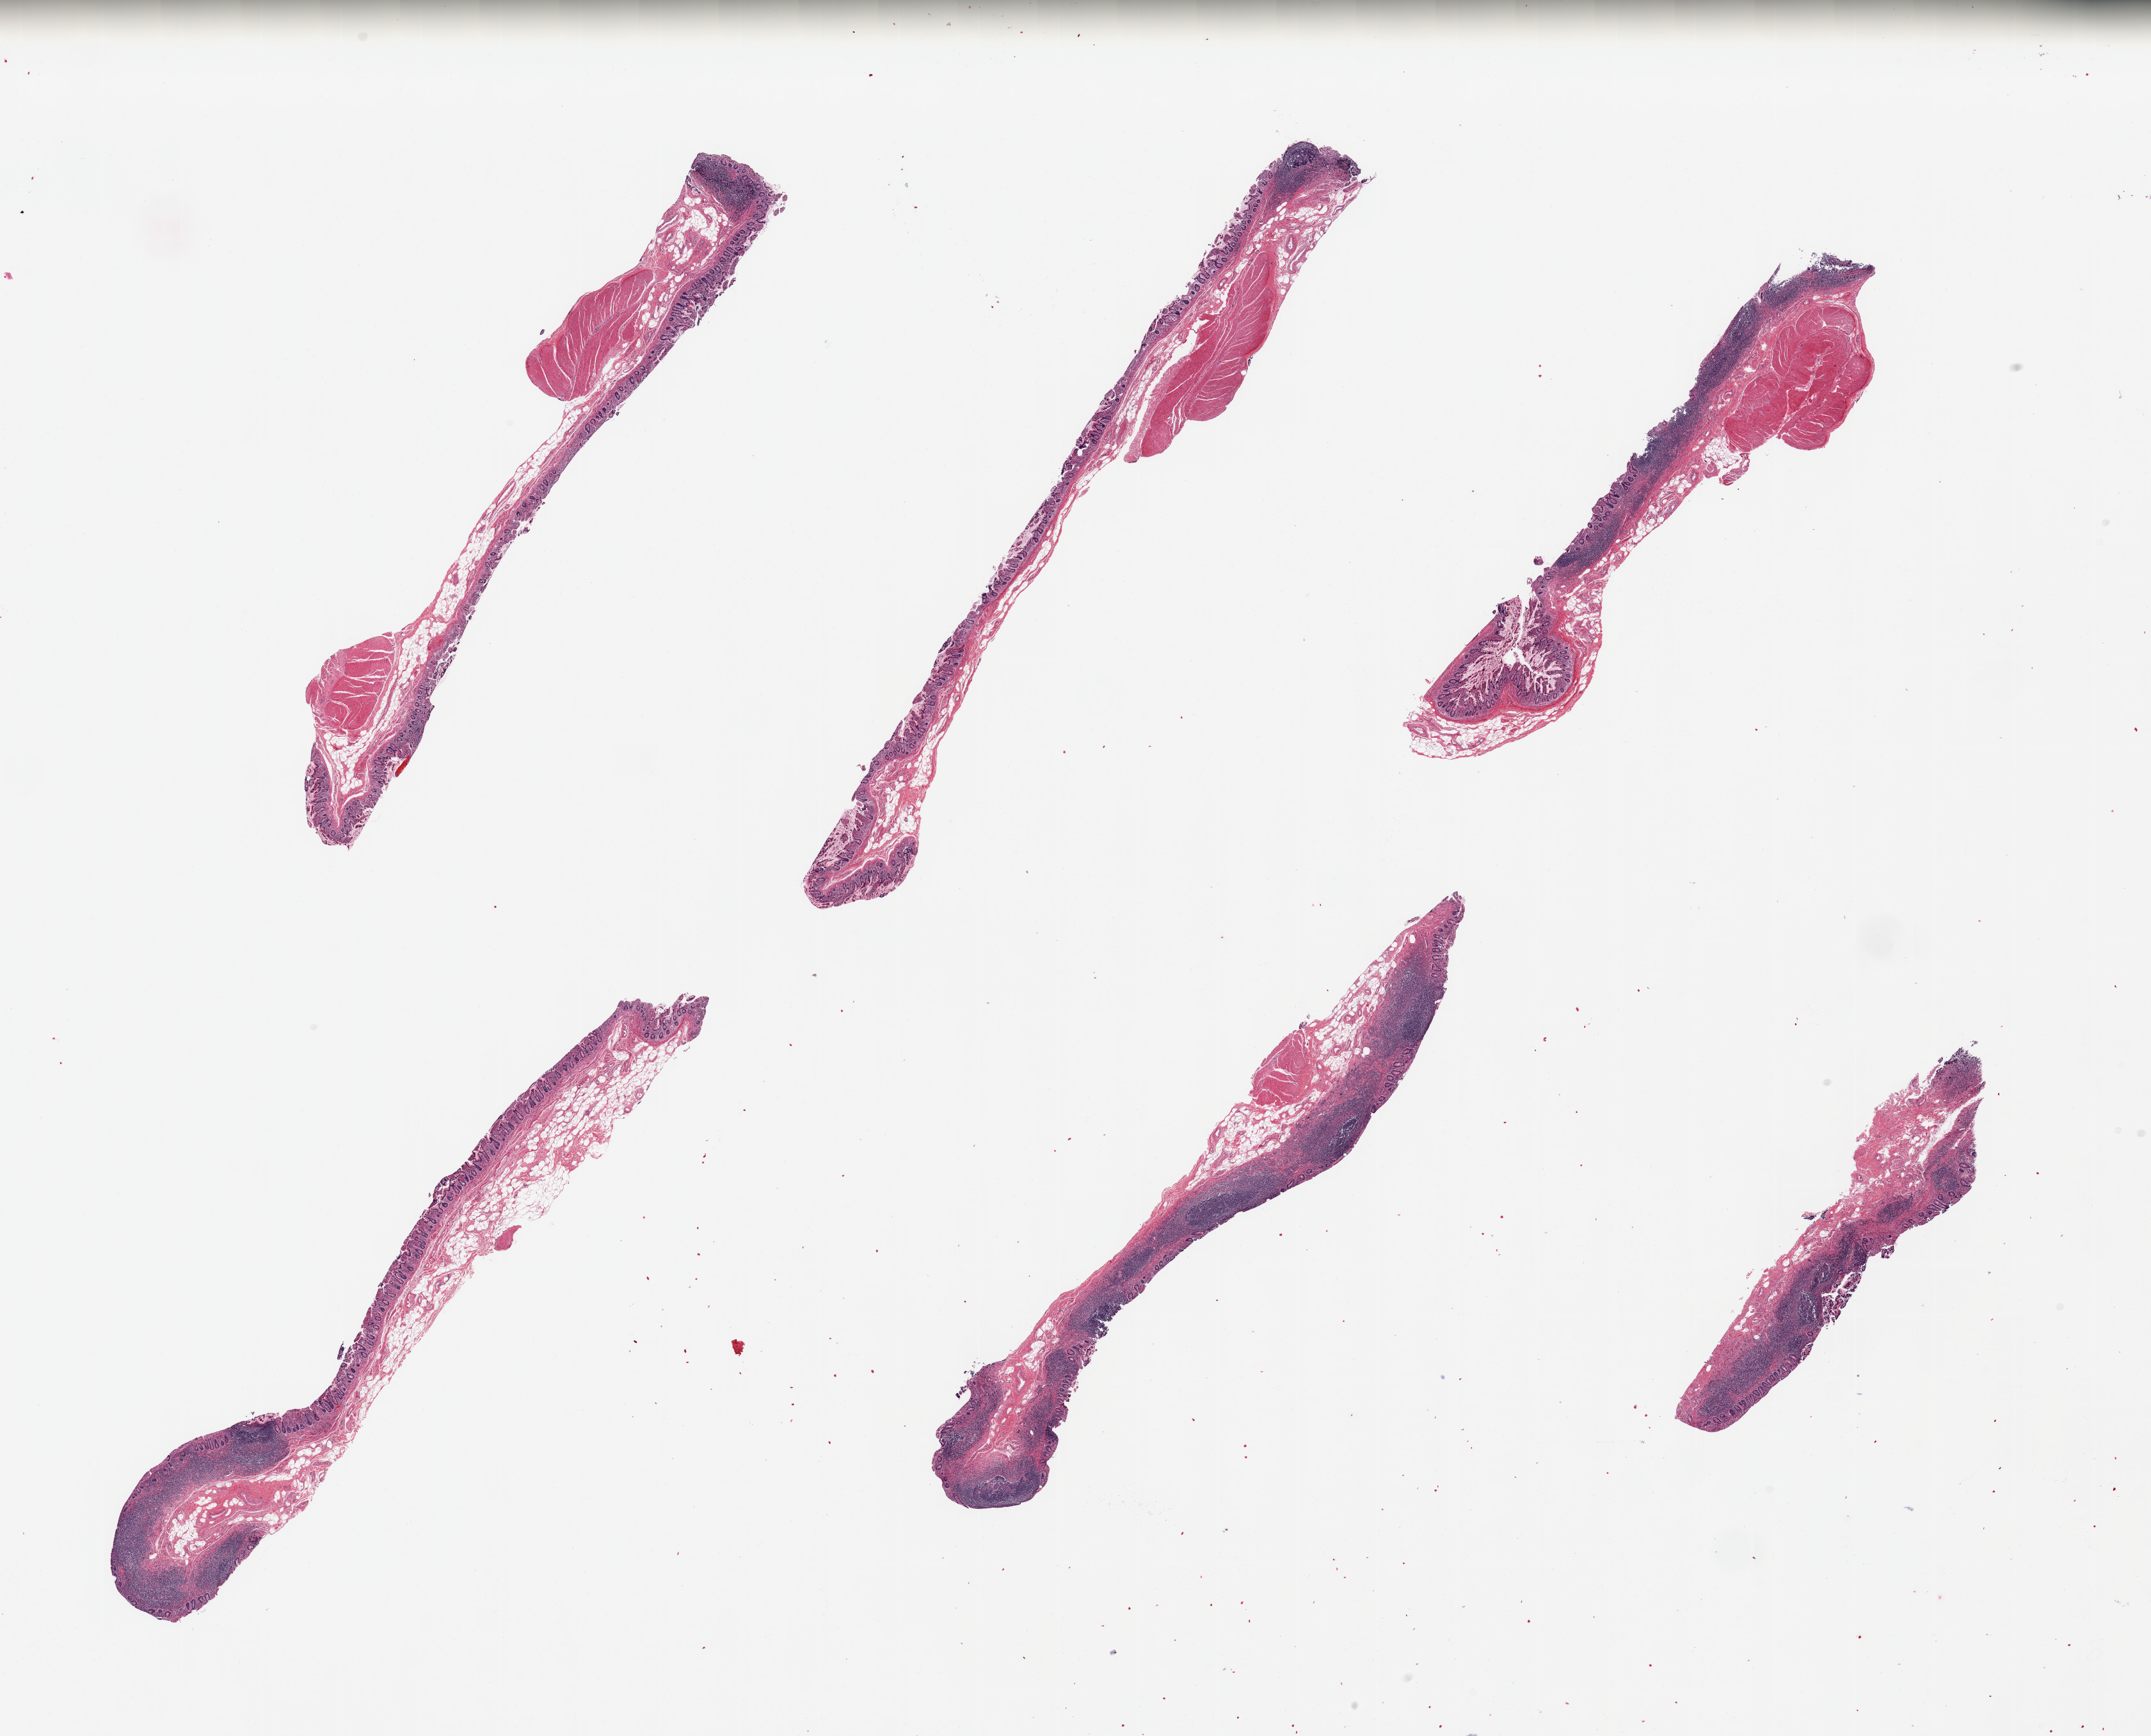
H&E whole-slide image, brightfield, shown as a low-resolution overview of the whole scanned area (about 26.6 x 21.5 mm); PAXgene-fixed, paraffin-embedded tissue; section of ileum (target tissue); donor tissue sample. Donor: male.
Reviewer comment on this tissue sample: 6 pieces; several include significant lymphoid tissue, few strips of residual musculairs.